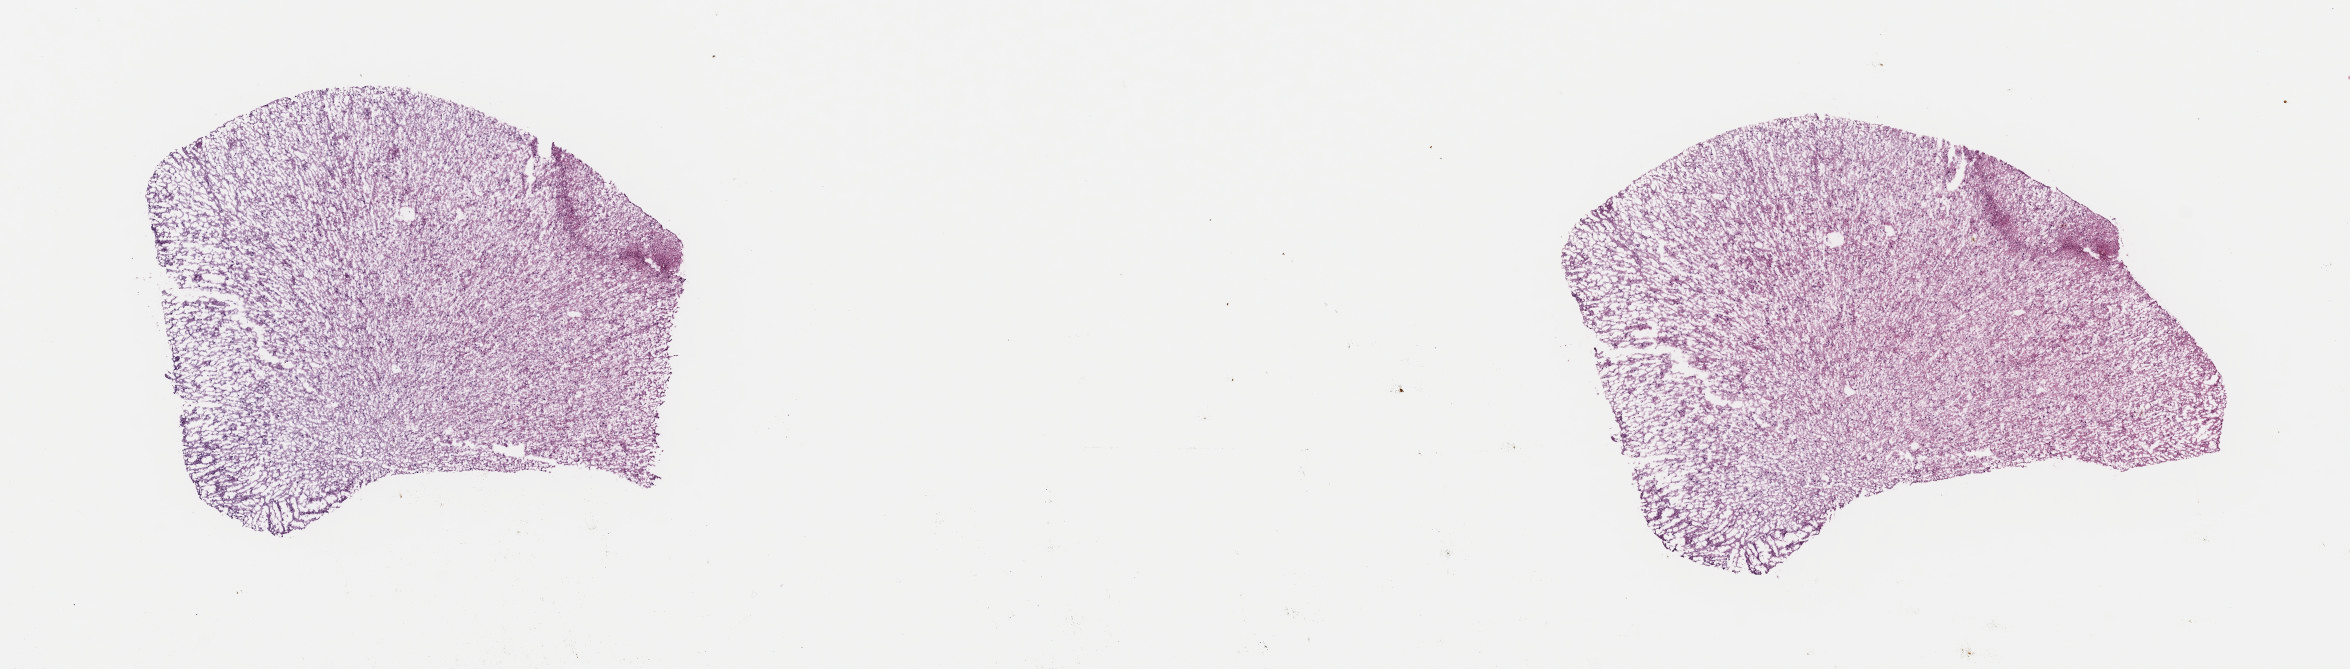
Hematoxylin and eosin (H&E) stained whole-slide image, whole scanned area (about 18.5 x 5.3 mm) shown as a low-resolution overview; frozen section from the top of the tissue portion; sample: primary tumour, brain. Patient: male, age at initial diagnosis 24 years. Histologic grade: G2 (moderately differentiated). Slide review estimates, as recorded: tumour cells 20%, tumour nuclei 80%, normal cells 10%, stromal cells 70%, necrosis 0%. Inflammatory infiltration, as recorded: lymphocyte infiltration 0%, monocyte infiltration 0%, neutrophil infiltration 0%.
Laterality: left. Histologic diagnosis: Astrocytoma, NOS (cerebrum).